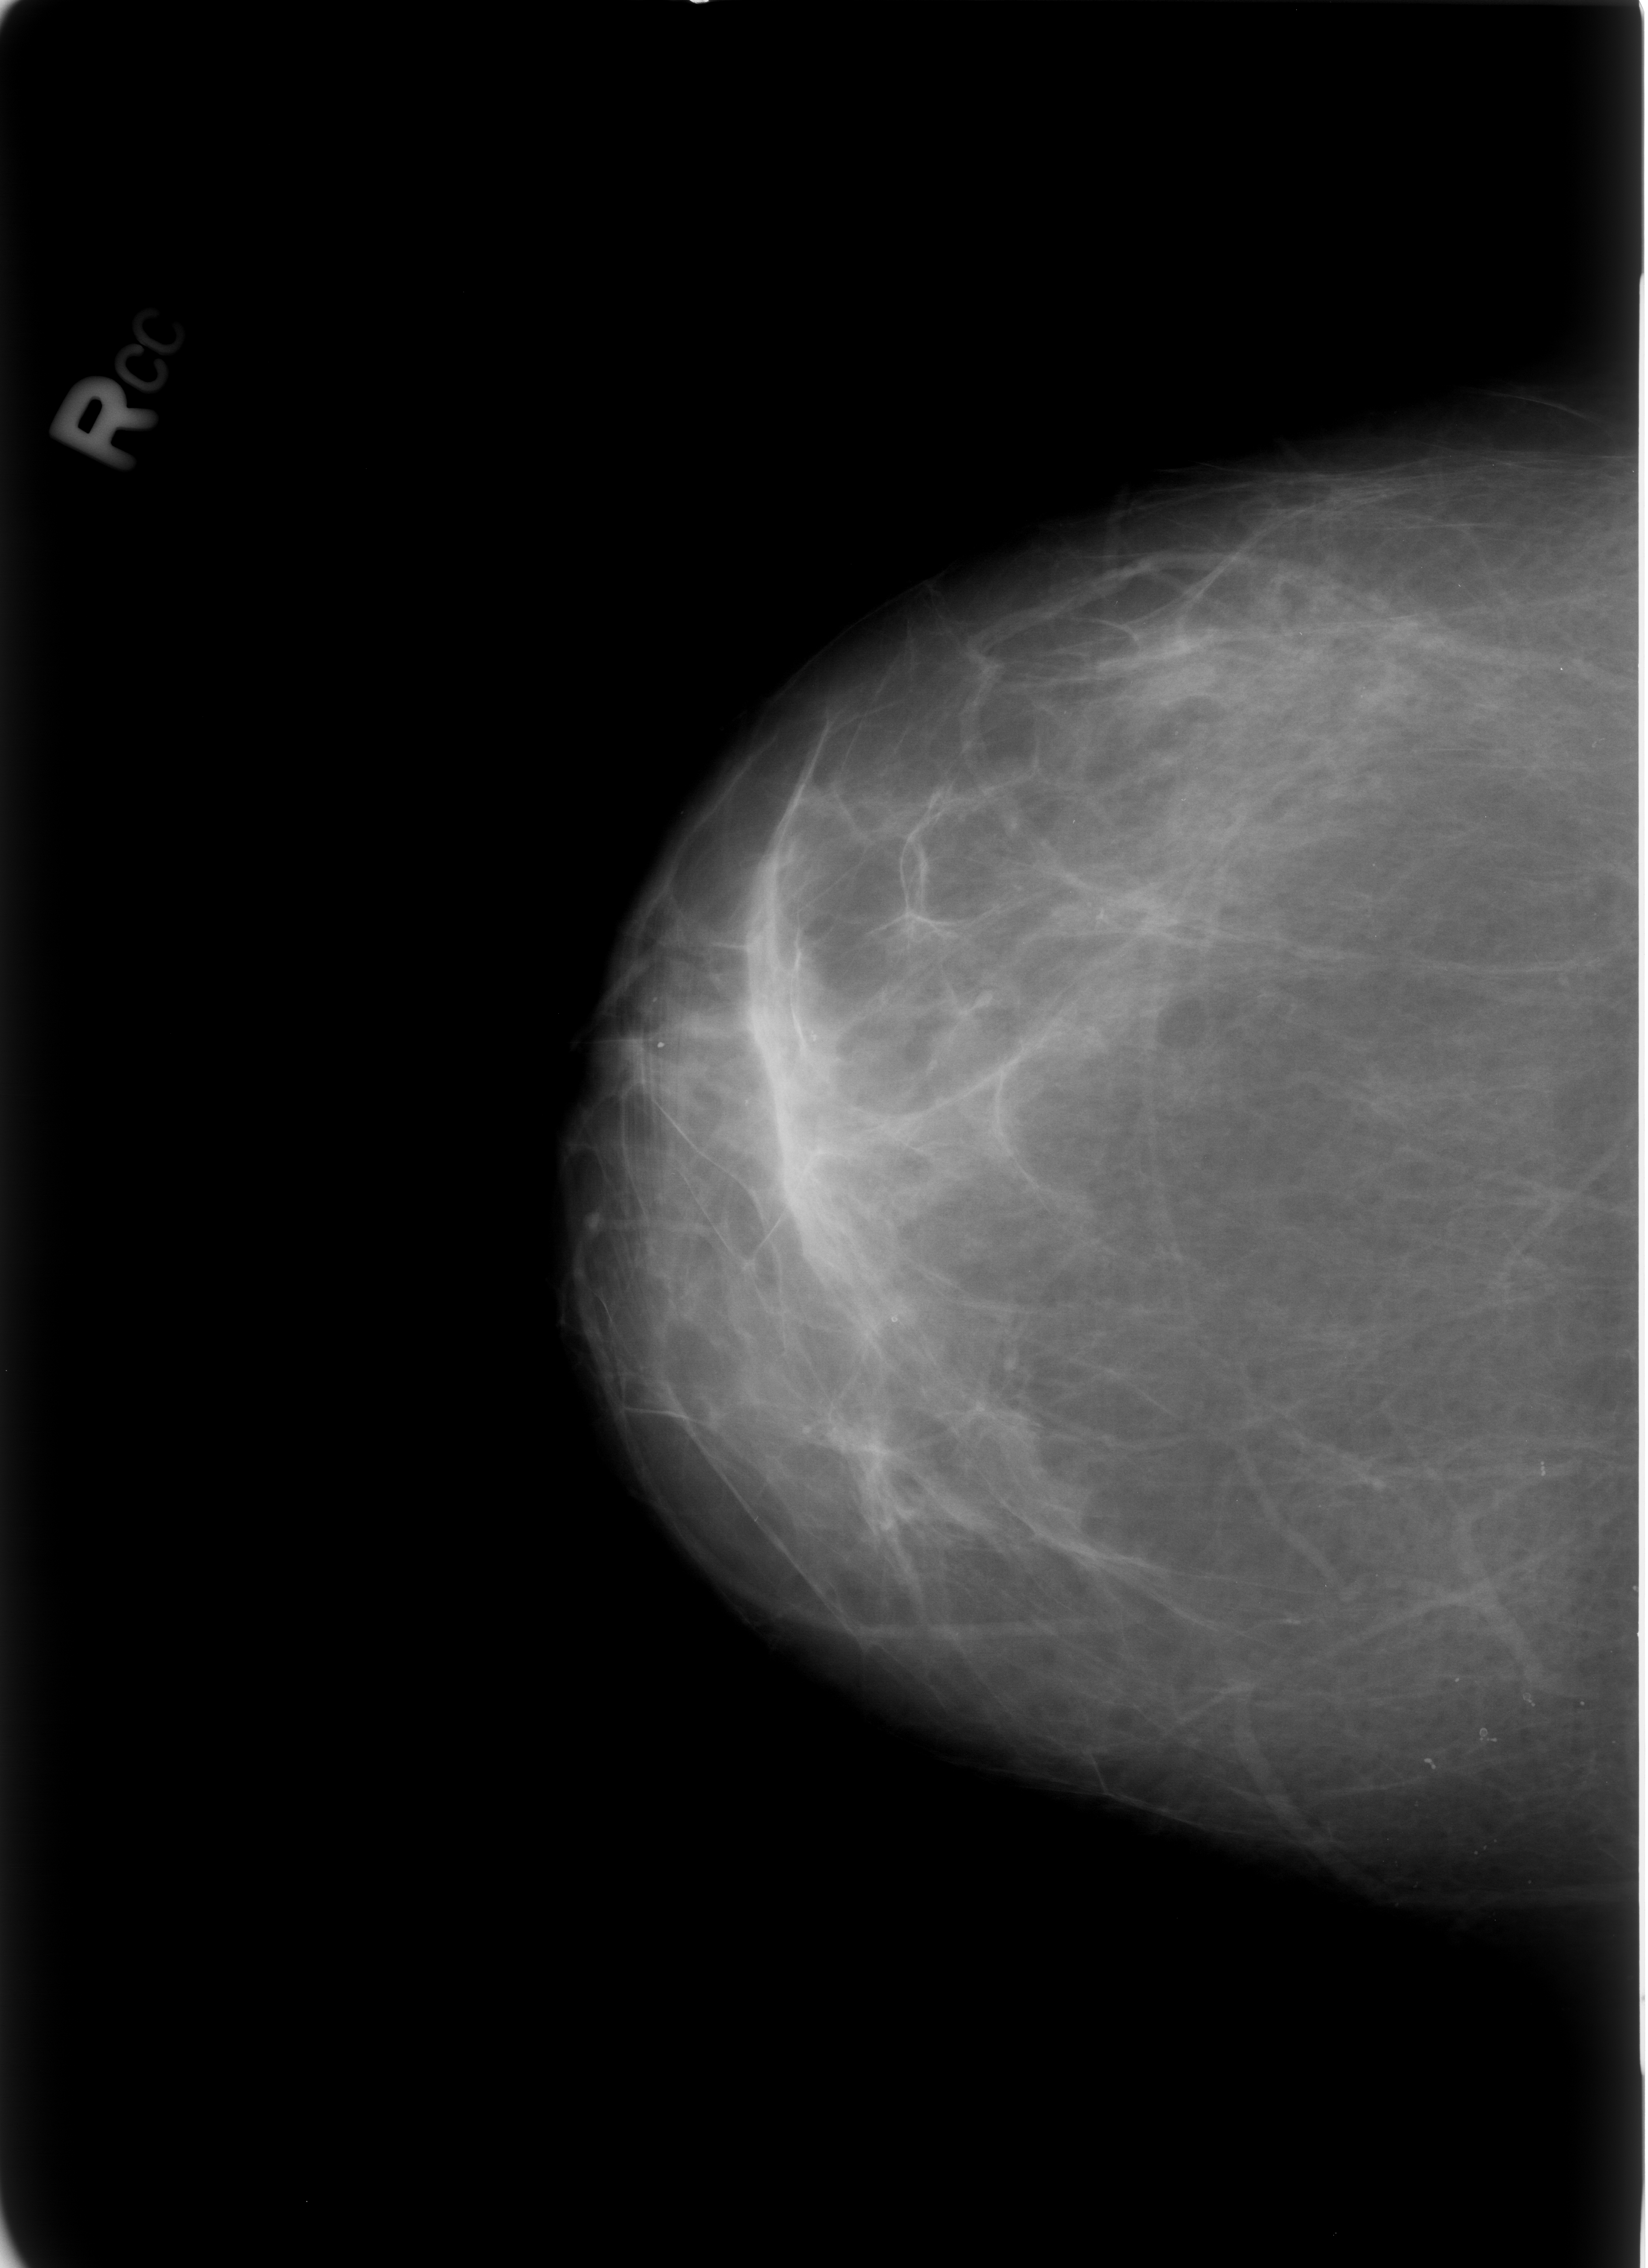
Mammogram (digitized film); right breast; CC view; BI-RADS breast density category 2 (scale 1–4); 1648 × 2268 image matrix.
Marked abnormalities (boxes around the expert regions of interest):
- calcifications, morphology skin, distribution regional; BI-RADS assessment category 2; subtlety rating 3 on a 1 (subtle) to 5 (obvious) scale; benign; no additional work-up was recommended (outcome (as recorded, no biopsy): benign without callback): bounding box (x1, y1, x2, y2) in pixels: (1467, 1712, 1497, 1752)